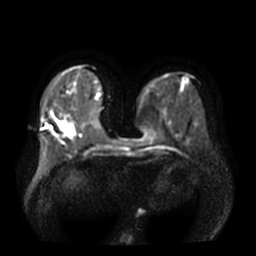
Breast MRI, one axial slice; position 12 of 36 along the scan axis; diffusion-weighted series; image 2 of 4 stored at this slice position (different b-values; order by instance number); 3 T; 5 mm slice thickness; 256 × 256 image matrix, field of view 360 × 360 mm. Female patient.
Annotated regions visible in this slice (manually delineated by an expert):
- tumour on diffusion-weighted imaging: bounding box [x1, y1, x2, y2] px = [64, 126, 73, 135]